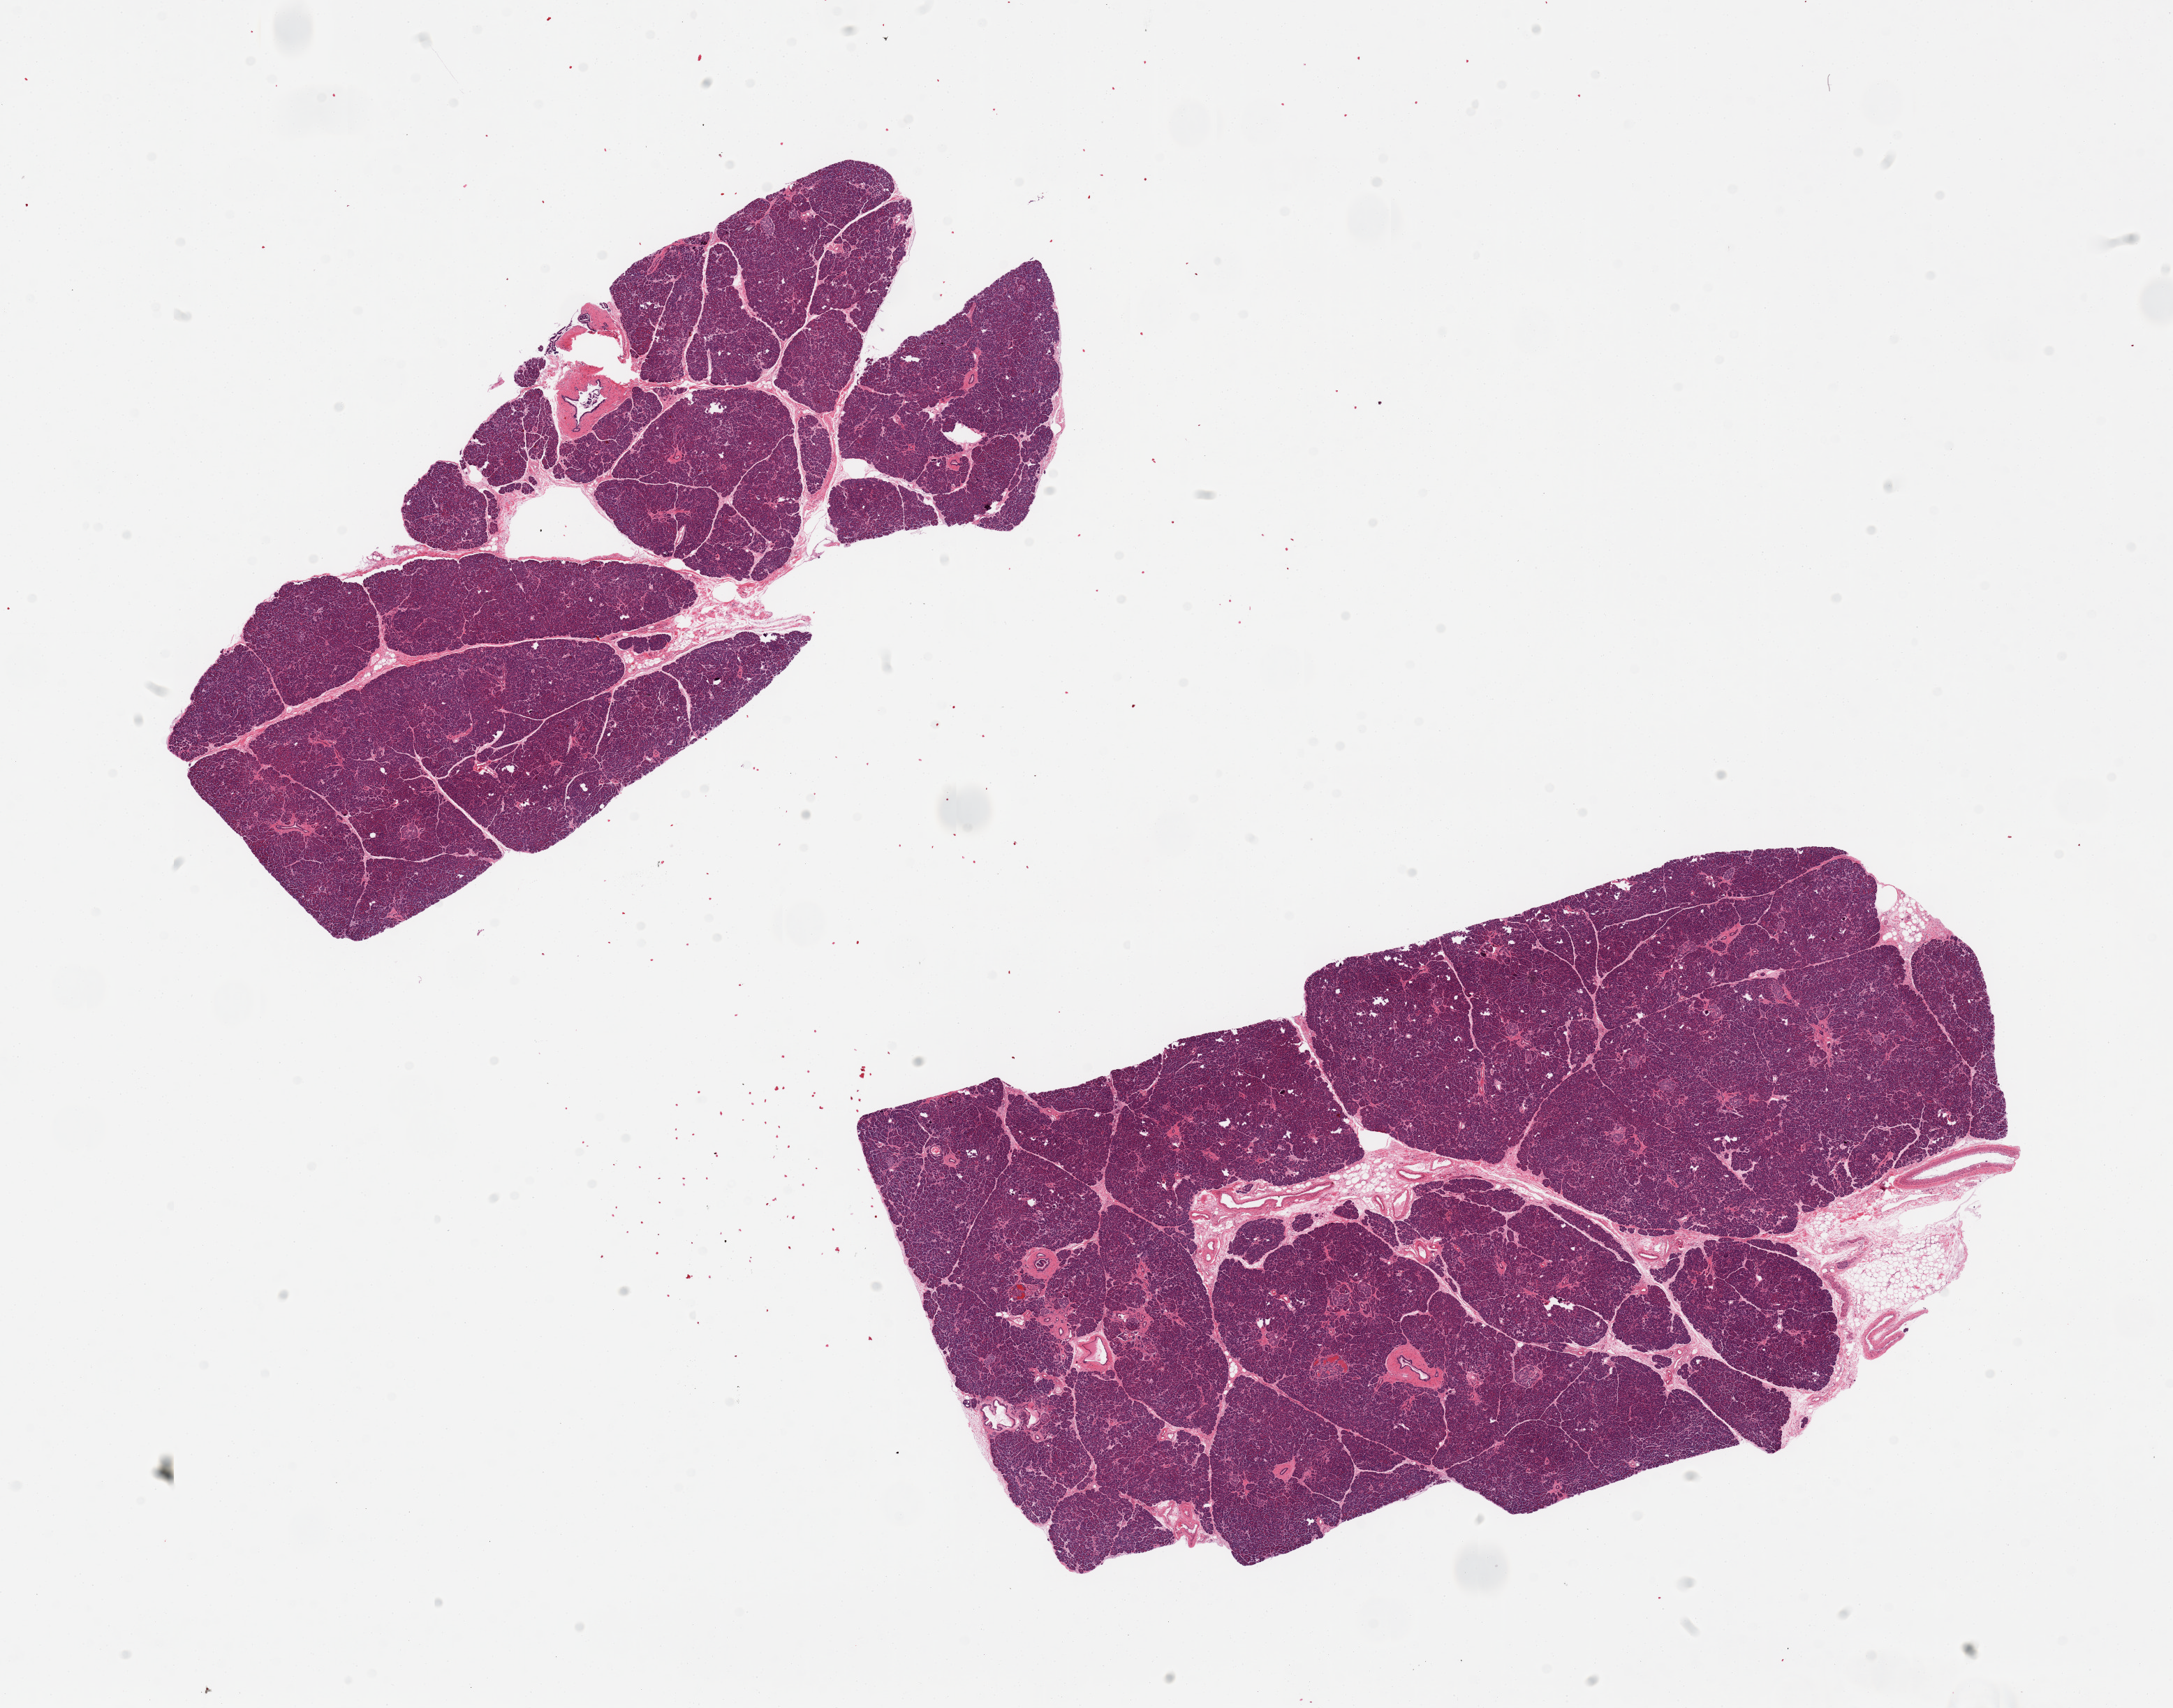
Digitized haematoxylin and eosin-stained section, whole scanned area (about 24.6 x 19.3 mm, slide scanned at 20x) shown as a low-resolution overview, PAXgene-fixed paraffin-embedded (PFPE) section, sampled site (target tissue): pancreas, donor tissue sample. Male donor.
Reviewer comment on this tissue sample: 2 pieces, no abnormalities.